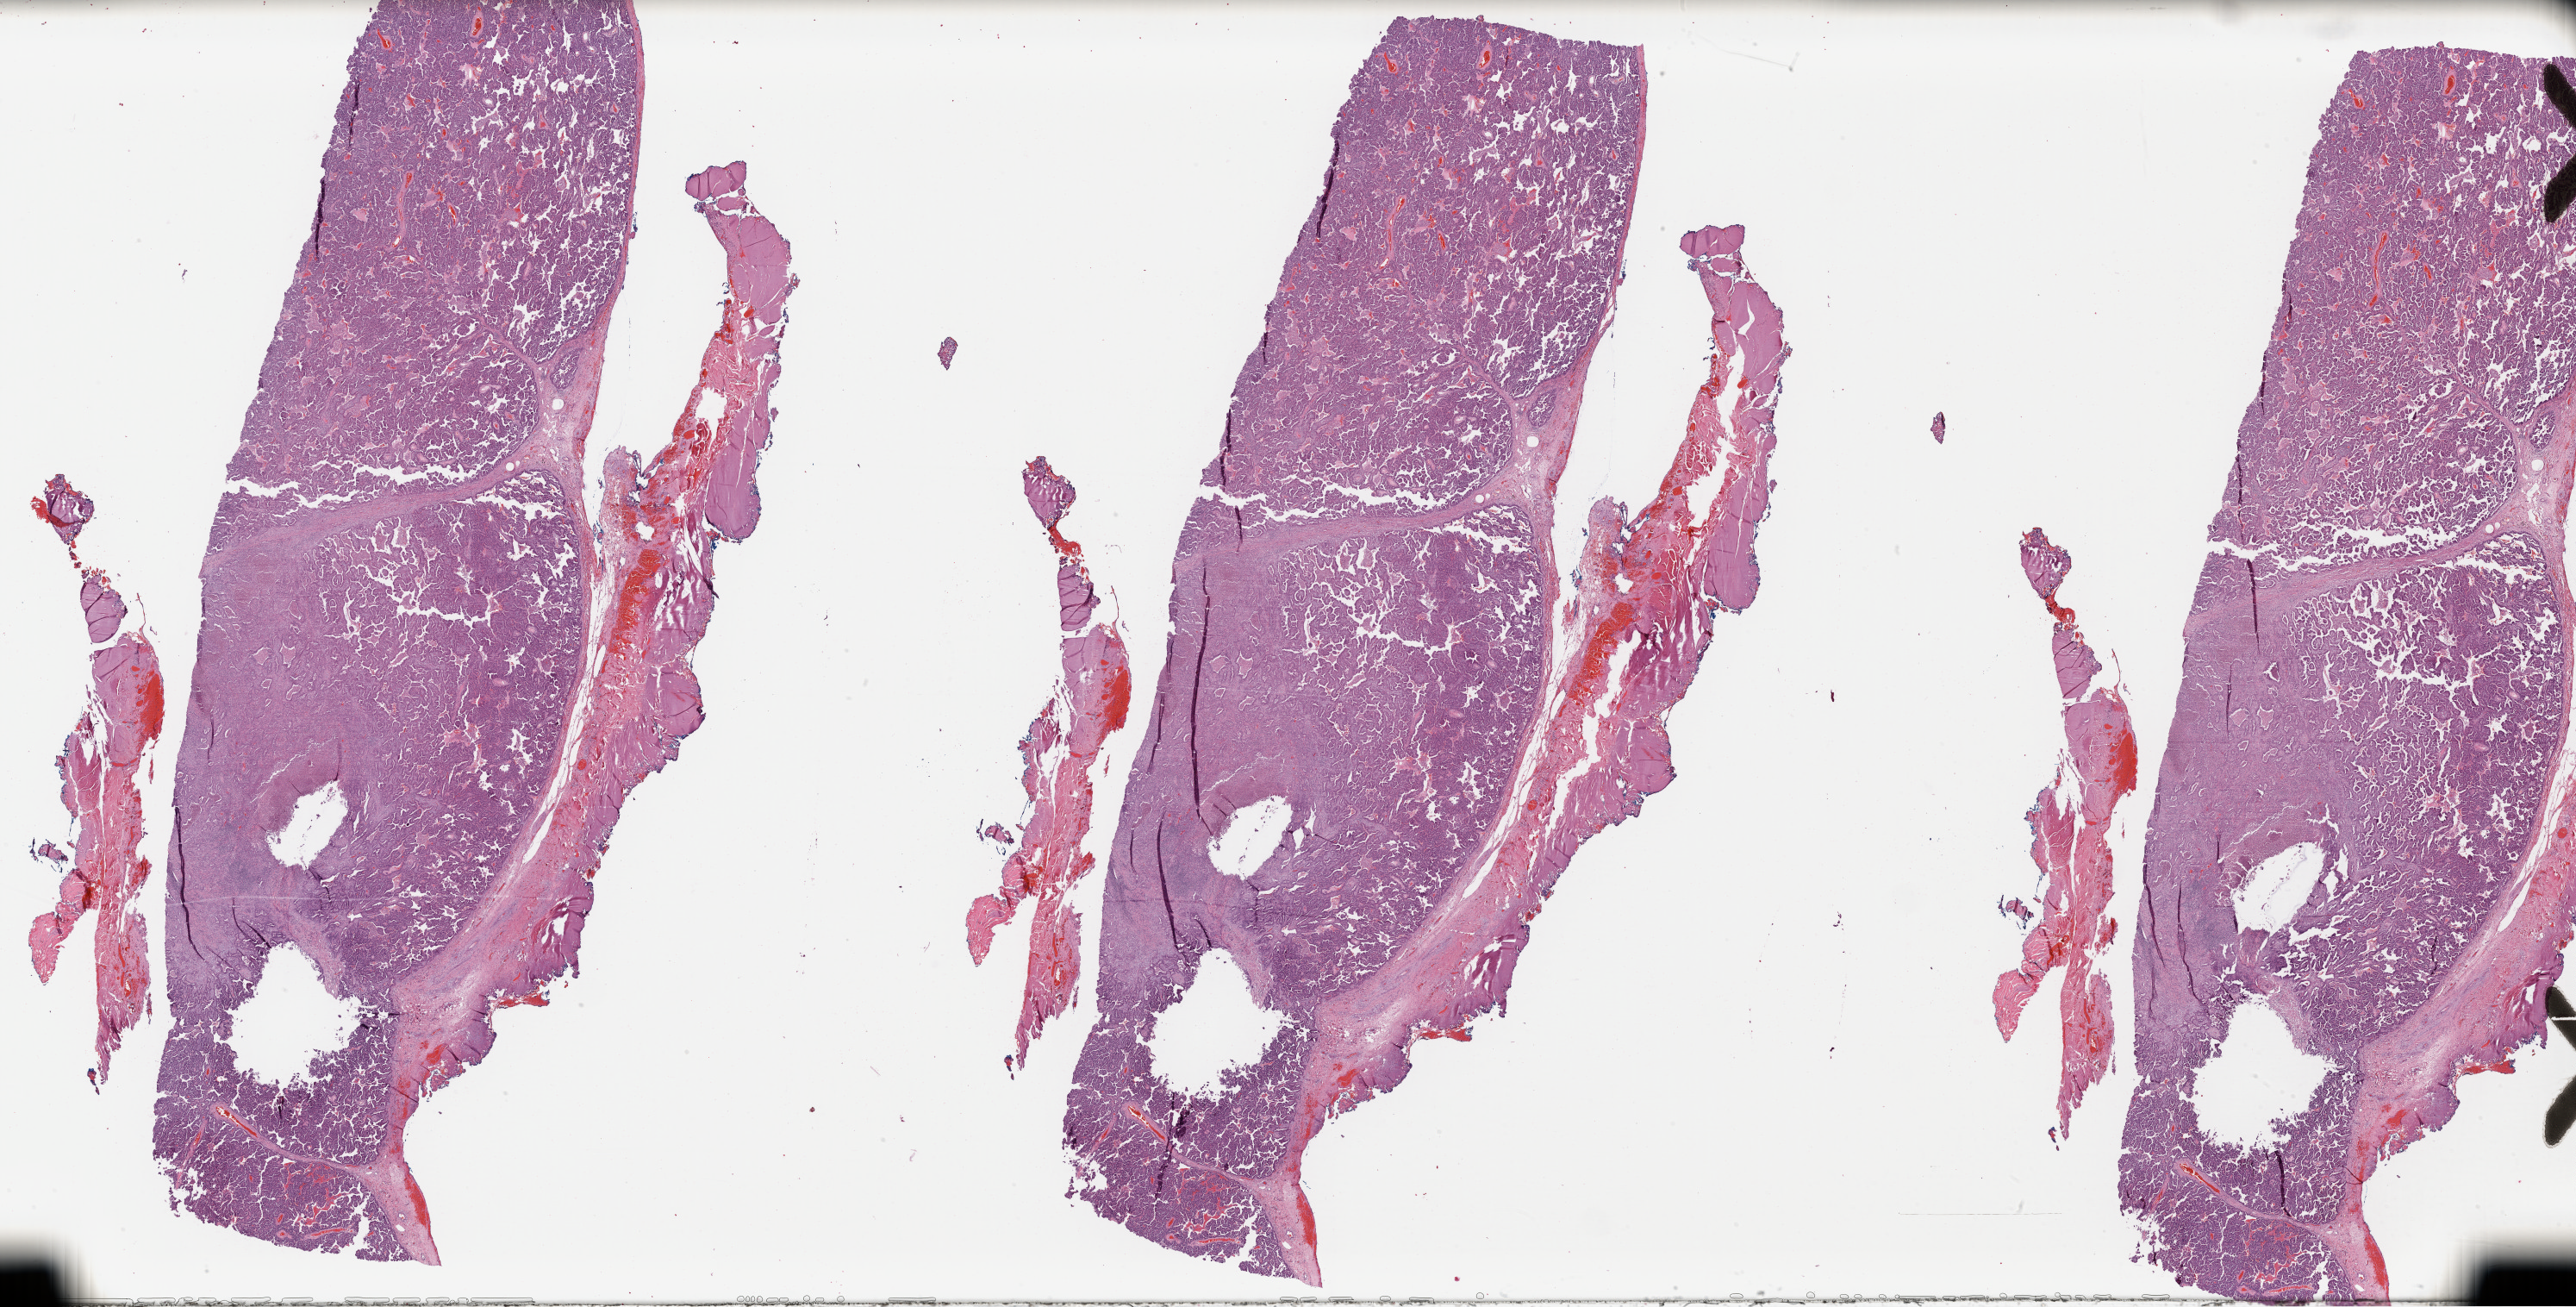
Hematoxylin and eosin (H&E) stained whole-slide image, shown as a low-resolution overview of the whole scanned area (about 47.0 x 23.8 mm), formalin-fixed paraffin-embedded (FFPE) diagnostic section, lung, primary tumour sample. Female, age 69 years at initial diagnosis.
* AJCC pathologic stage: IIB (7th edition)
* pathologic diagnosis: Adenocarcinoma with mixed subtypes (lower lobe, lung)